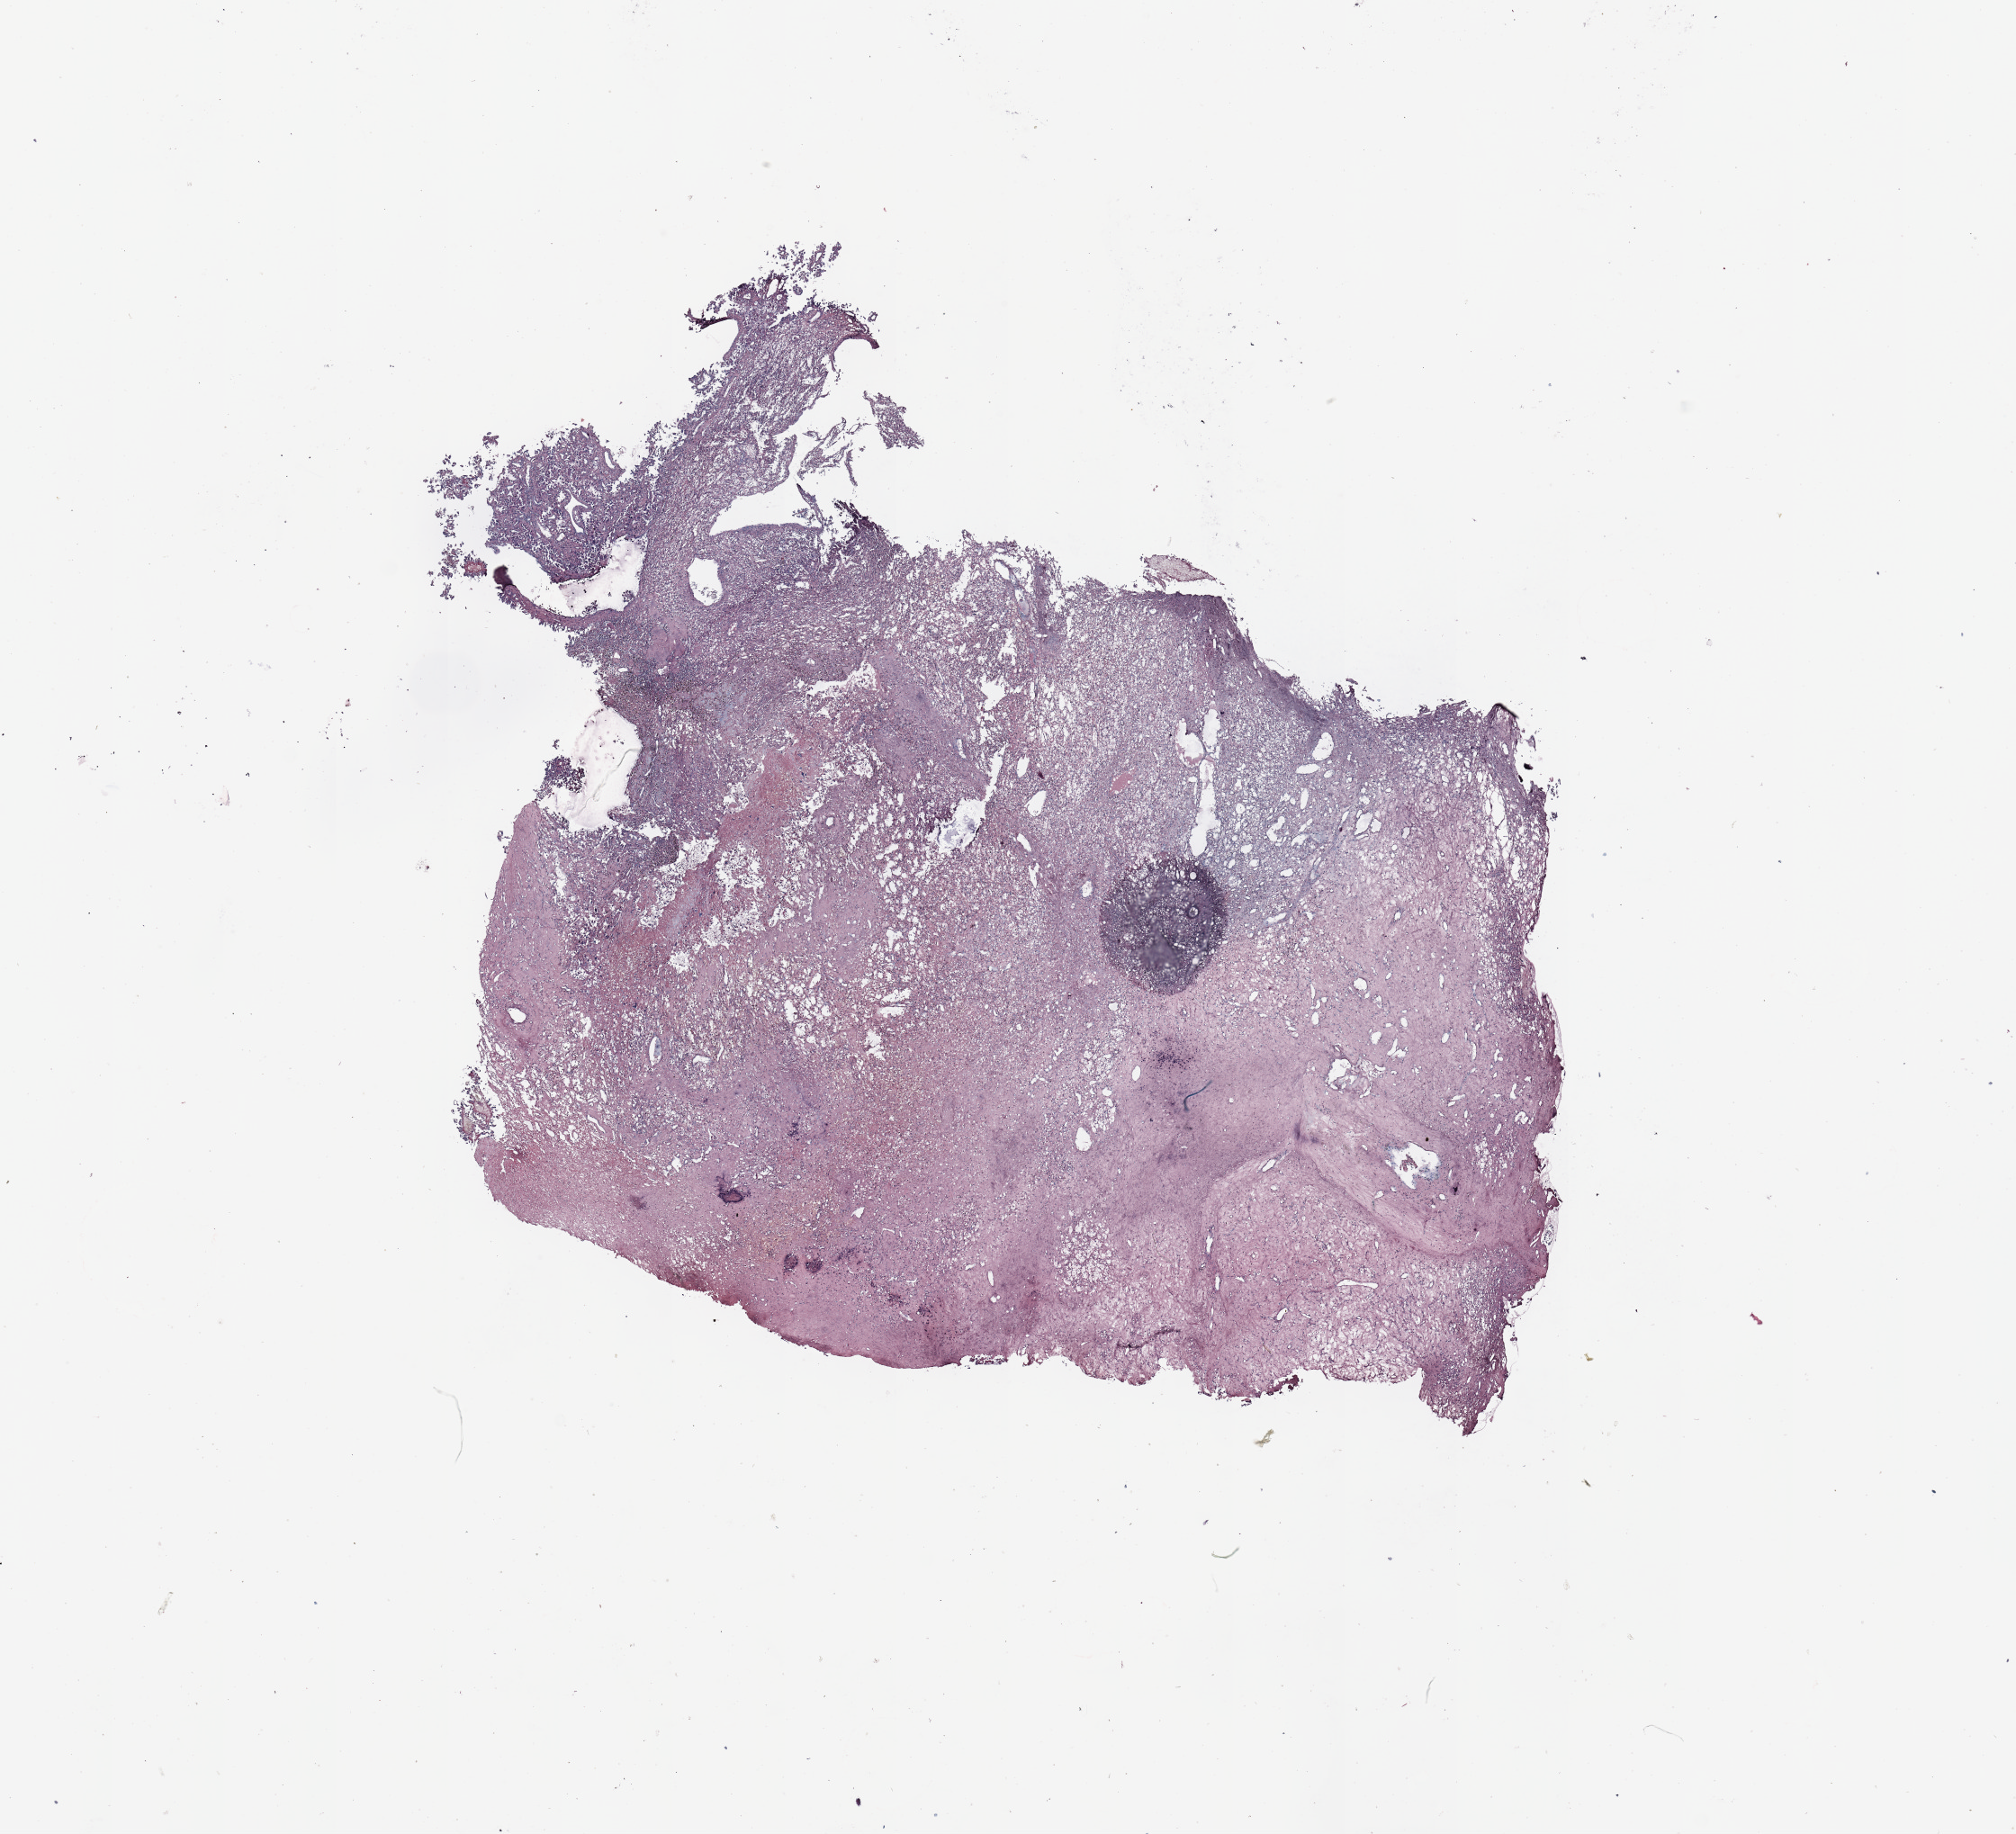
Whole-slide histology image, H&E-stained, whole scanned area (about 17.7 x 16.1 mm, slide scanned at 20x) shown as a low-resolution overview, tumour tissue sample, sampled site: kidney. 56-year-old female patient.
Diagnosis: Renal cell carcinoma, NOS.